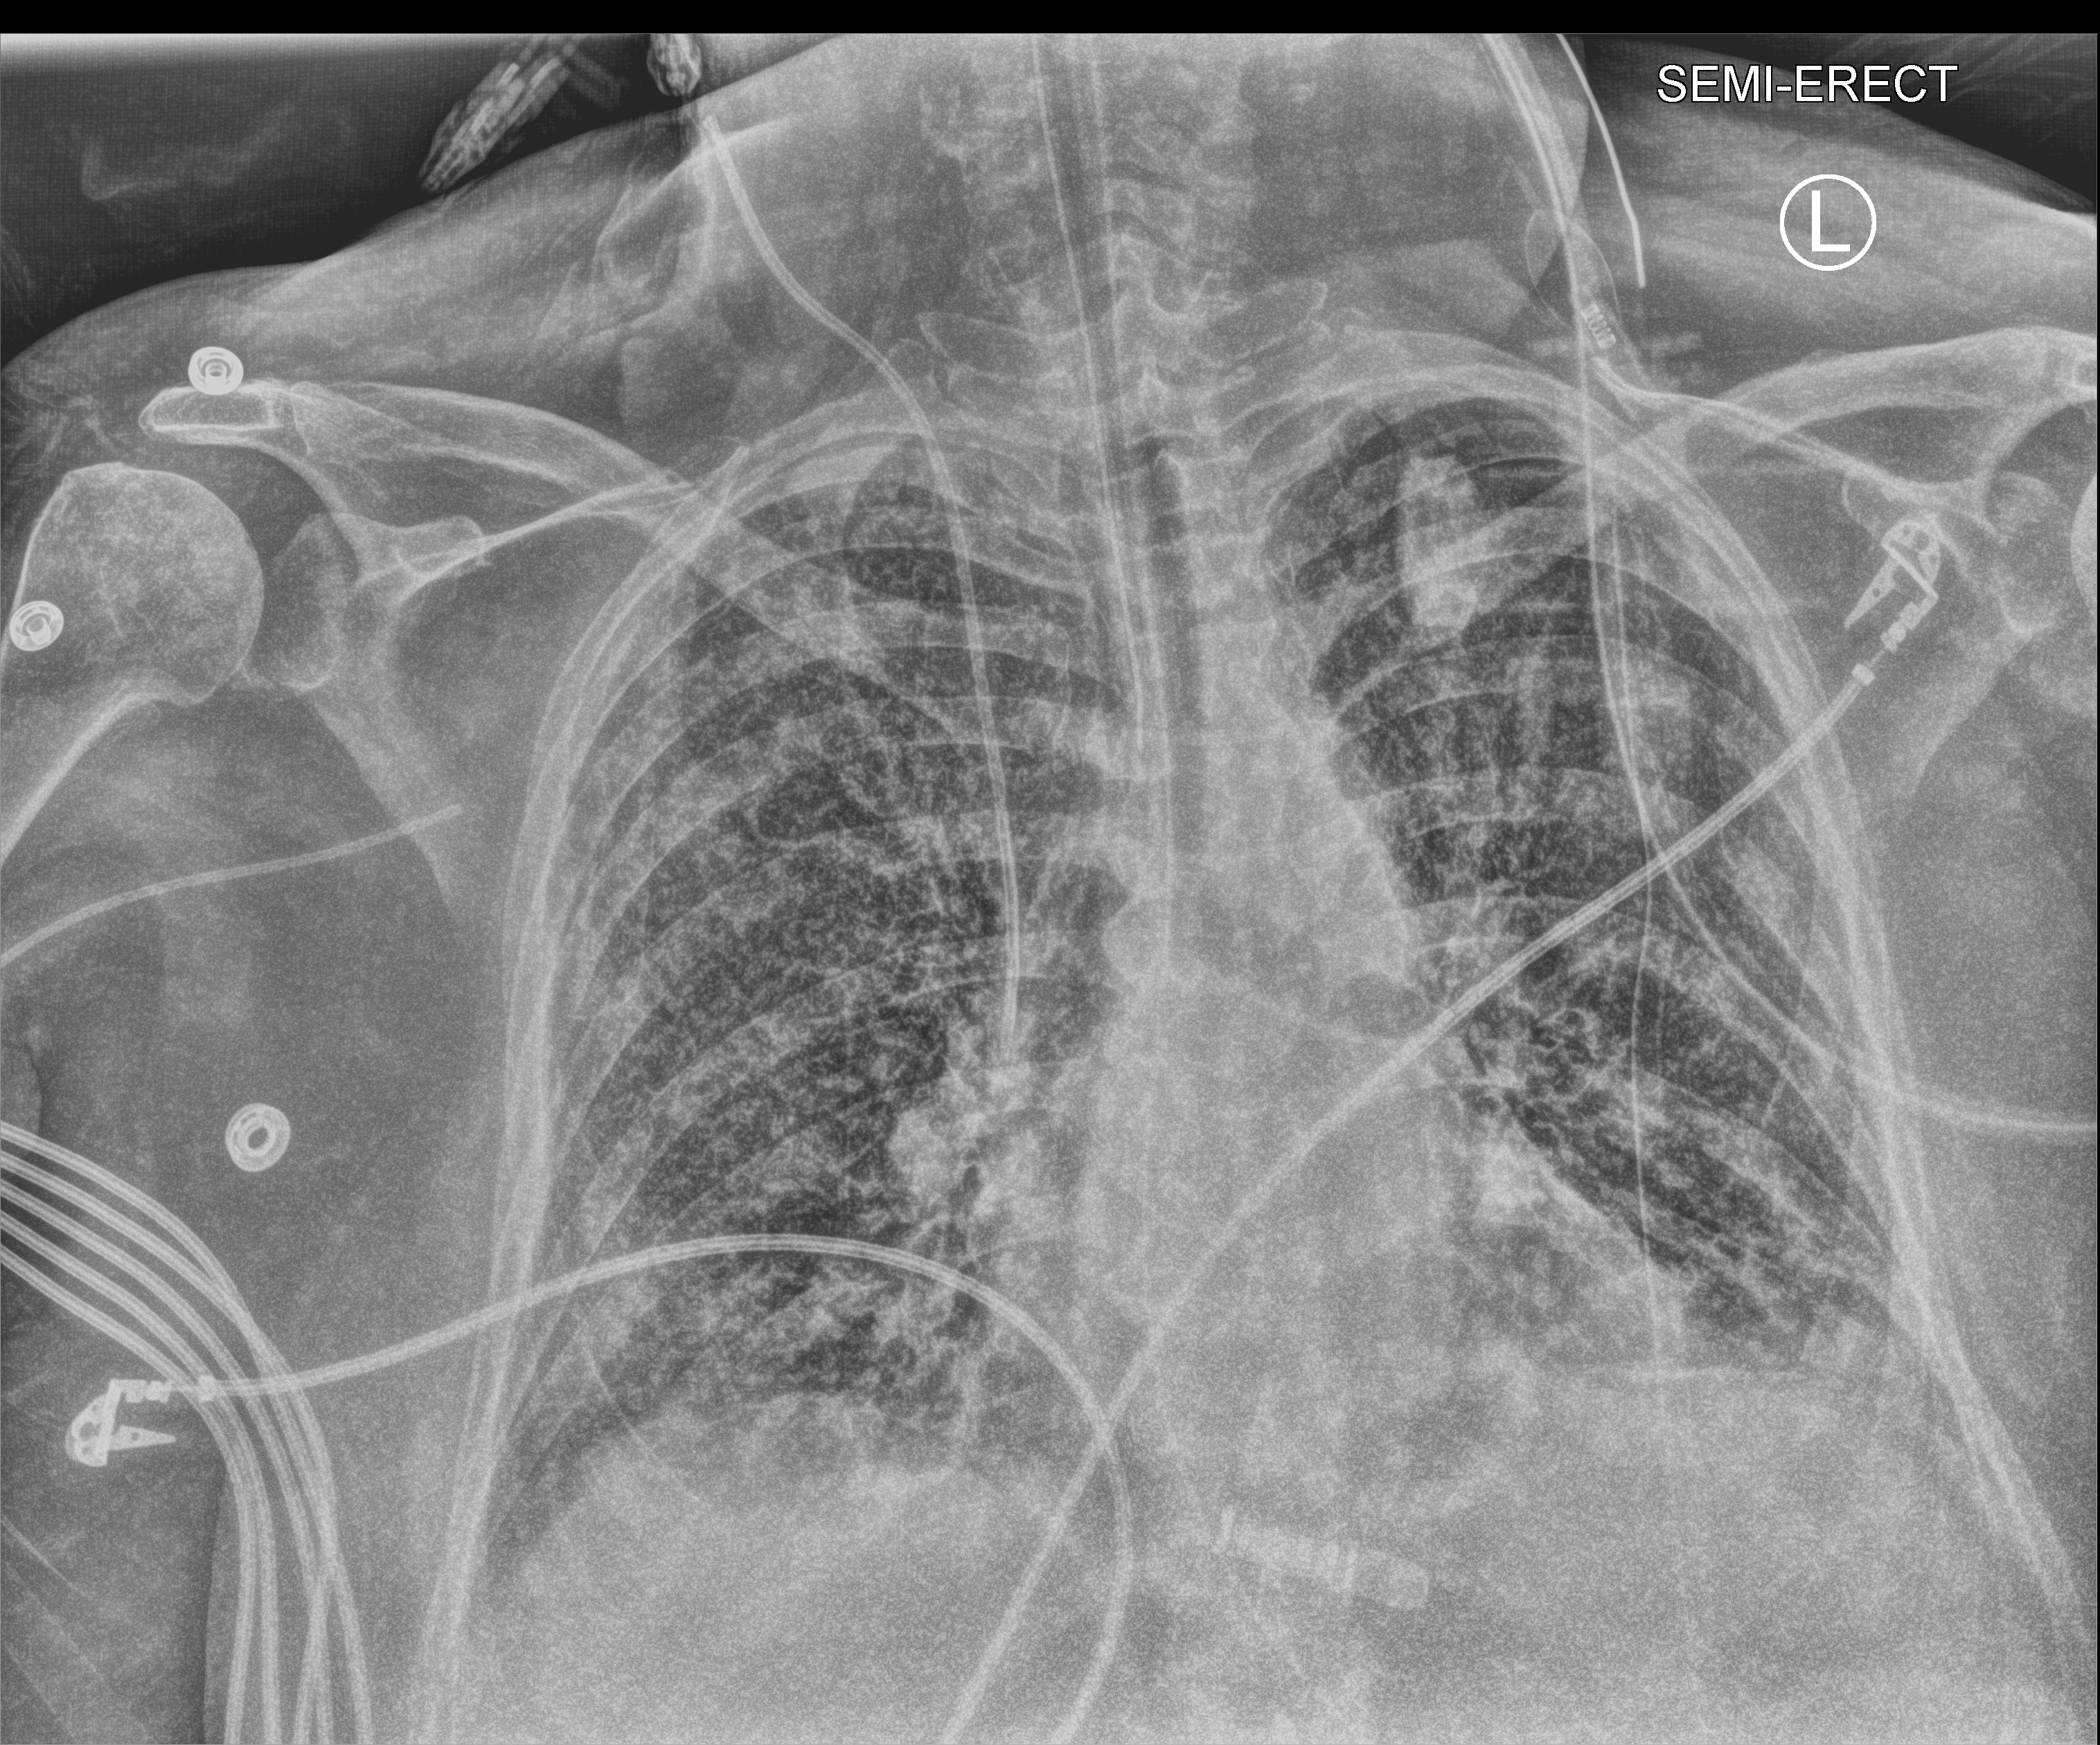
Chest X-ray (portable); anteroposterior (AP) projection. Patient hospitalised with COVID-19; female, aged 60–74 years.
From the hospital-stay record, not from the radiograph (when in the stay this image was taken is not recorded): admitted to intensive care during this hospital stay: yes; mechanically ventilated during this hospital stay: yes.